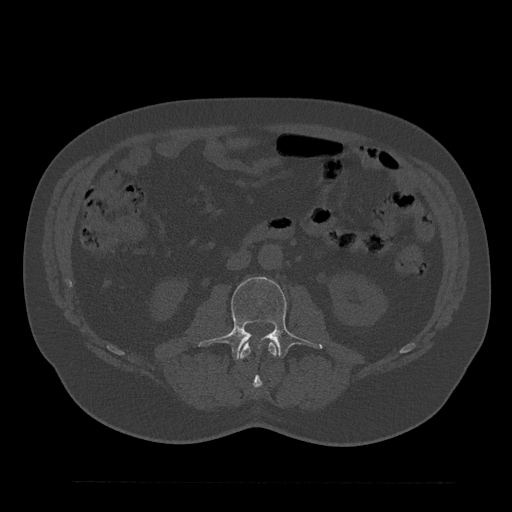
CT including the spine, one axial slice; slice 51 of 797 in the series (ordered by position); reconstruction kernel Br40s/3; 120 kVp; bone window (W 1800 / L 400 HU); 0.5 mm slice thickness; 512 × 512 image matrix. Patient: male, 61 years. Case-level facts recorded for this patient, not image findings: primary cancer: prostate.
Outlined on this slice (semi-automatically segmented with operator editing):
- L2 vertebra: bounding box (x1, y1, x2, y2) in pixels: (239, 342, 278, 397)
- L3 vertebra: (199, 277, 322, 360)